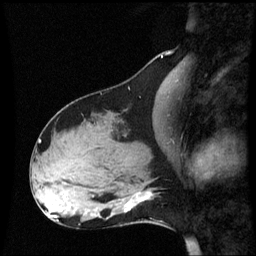
Breast MRI (dynamic contrast-enhanced), one sagittal slice. Position 24 of 60 along the scan axis. Dynamic contrast-enhanced series, image 2 of 3 at this slice position (ordered by acquisition). 1.5 T. TE 4.2 ms, TR 8.9 ms. 2.2 mm slice thickness. 256 × 256 image matrix. Patient: female, 31 years. Case-level facts recorded for this patient, not image findings: setting: breast cancer imaged before/during neoadjuvant chemotherapy; receptor status: HR-positive, HER2-negative.
Structures marked on this image (semi-automatic segmentation, software-assisted and operator-edited):
- analysis volume of interest (the breast-tissue region the enhancement analysis was run in; not a lesion): bounding box [x1, y1, x2, y2] px = [109, 180, 159, 227]
- tumour enhancement mask (voxels above the 70 % enhancement threshold inside the analysis volume of interest): [127, 208, 129, 211]